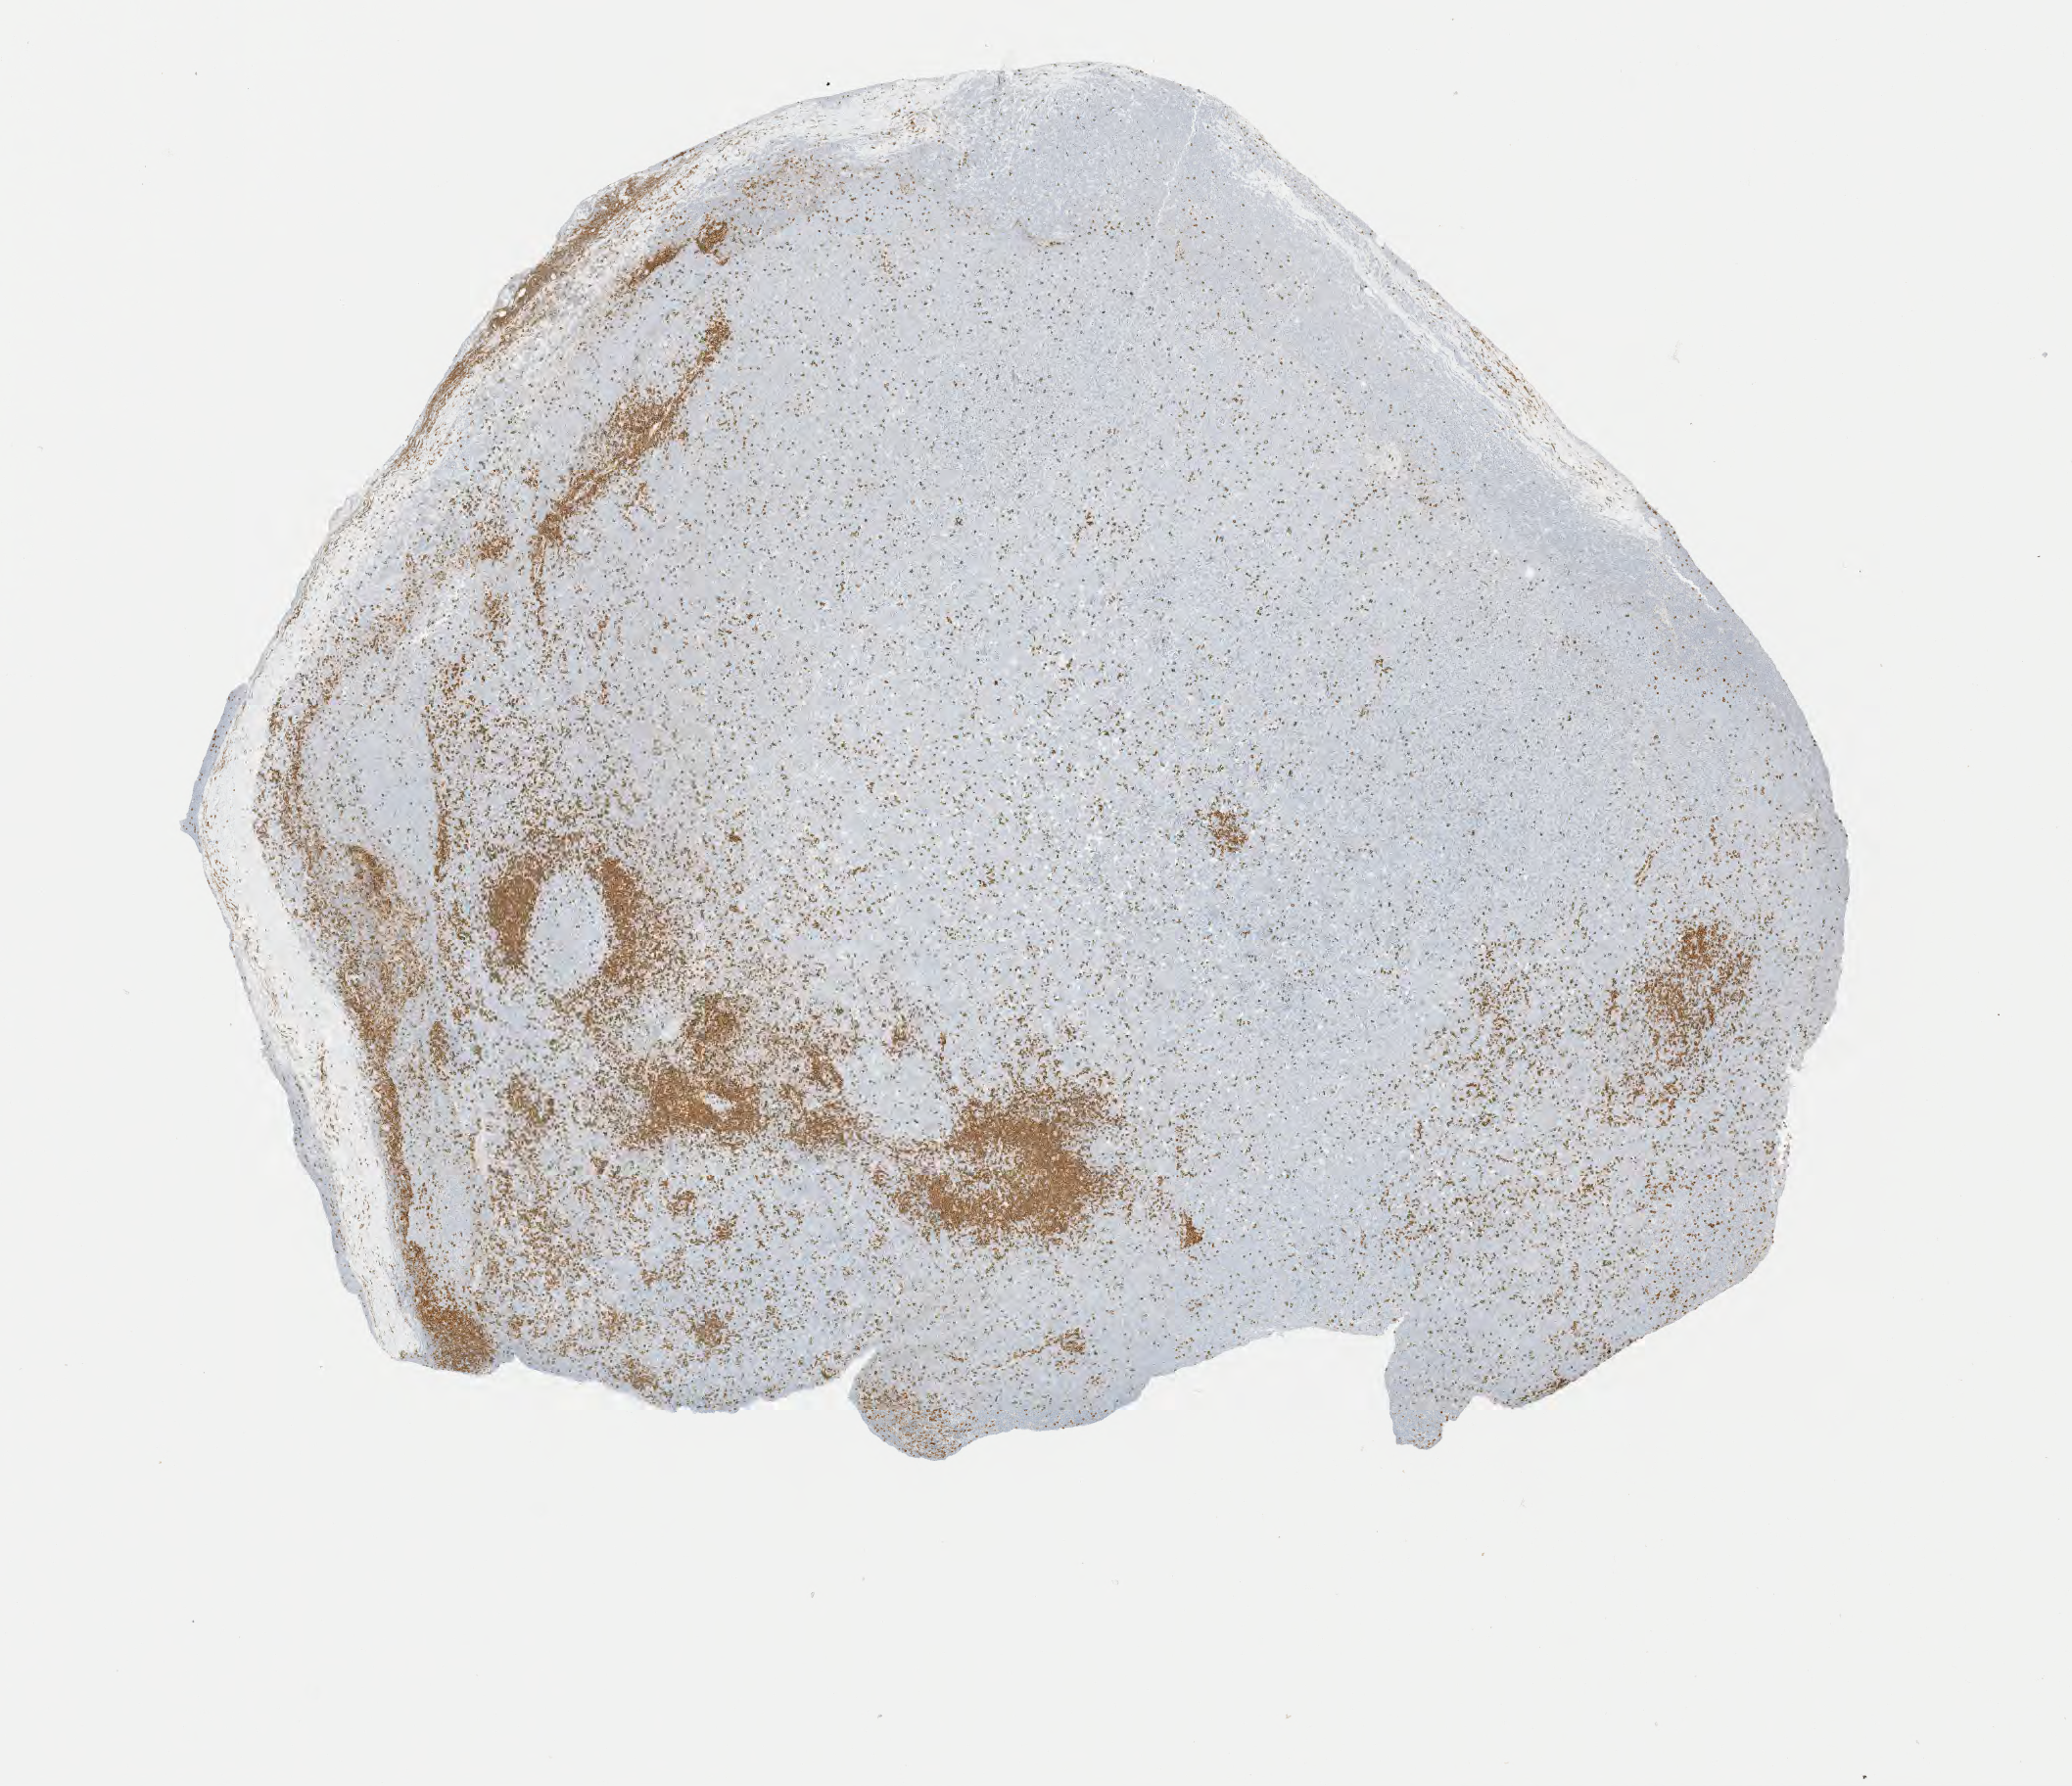
IHC for CD3, whole-slide image, a low-resolution overview of the entire scanned area, about 8.6 x 7.4 mm. Specimen: tumor tissue. Patient: male, aged 45.
Diagnosis: Burkitt lymphoma, NOS.